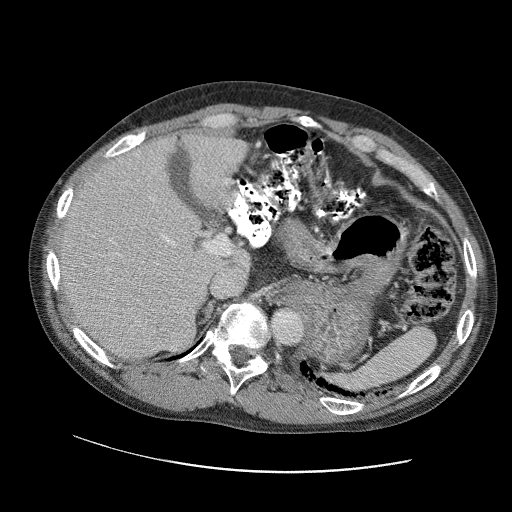
Contrast-enhanced abdominal CT (liver protocol), one axial slice. Position 70 of 109 along the scan axis. Reconstruction kernel STANDARD. 120 kVp. Soft-tissue window (W 400 / L 40 HU). 2.5 mm slice thickness. 512 × 512 image matrix, field of view 400 × 400 mm. From the clinical record (not read from this slice): diagnosis: hepatocellular carcinoma (patient treated with transarterial chemoembolisation; whether this scan precedes or follows treatment is not stated here); TNM stage (as recorded): Stage-IIIC; Child-Pugh class: B; tumour differentiation: well differentiated; tumour nodularity: uninodular.
Annotated regions visible in this slice (semi-automatically segmented with operator editing):
- liver parenchyma outside the tumour (the mass and vessels are separate outlines, so this box may not span the whole liver): box from (x=56, y=128) to (x=250, y=360) px
- mass: (x=158, y=316)–(x=193, y=352)
- liver vessels: (x=72, y=172)–(x=238, y=302)